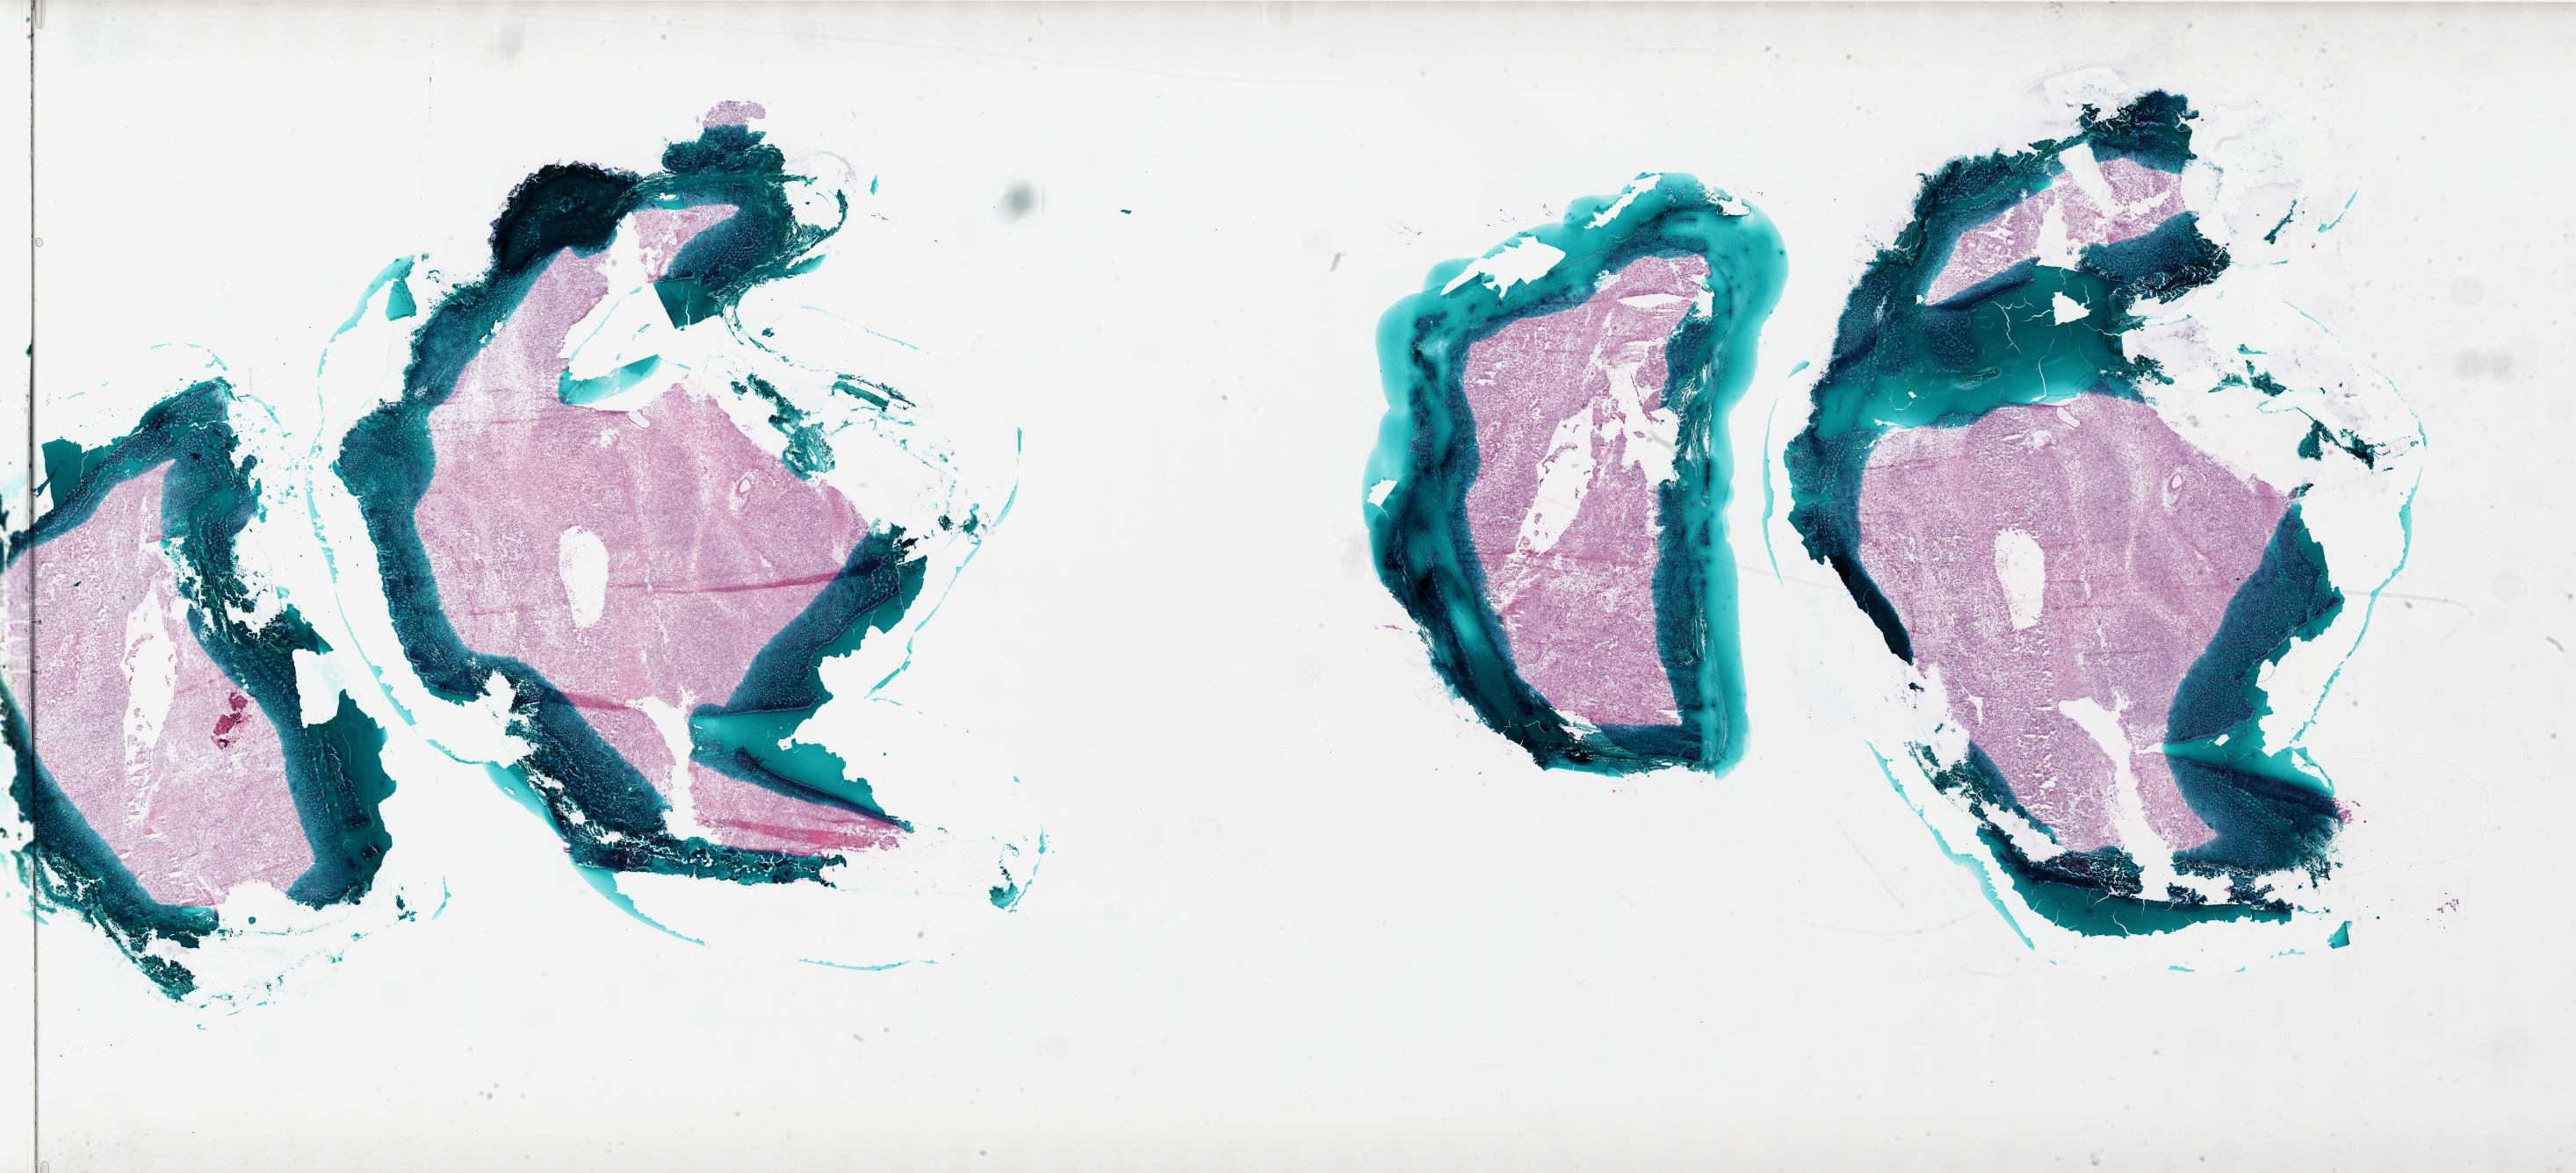
Hematoxylin and eosin (H&E) stained whole-slide image, low-resolution overview of the scanned area, about 47.0 x 21.4 mm; frozen section; sample: primary tumour, brain. Patient: male, age at initial diagnosis 49 years. Composition of this section per pathologist review: tumour cells 90%, tumour nuclei 100%, normal cells 0%, stromal cells 0%, necrosis 10%.
Pathologic diagnosis: Glioblastoma.